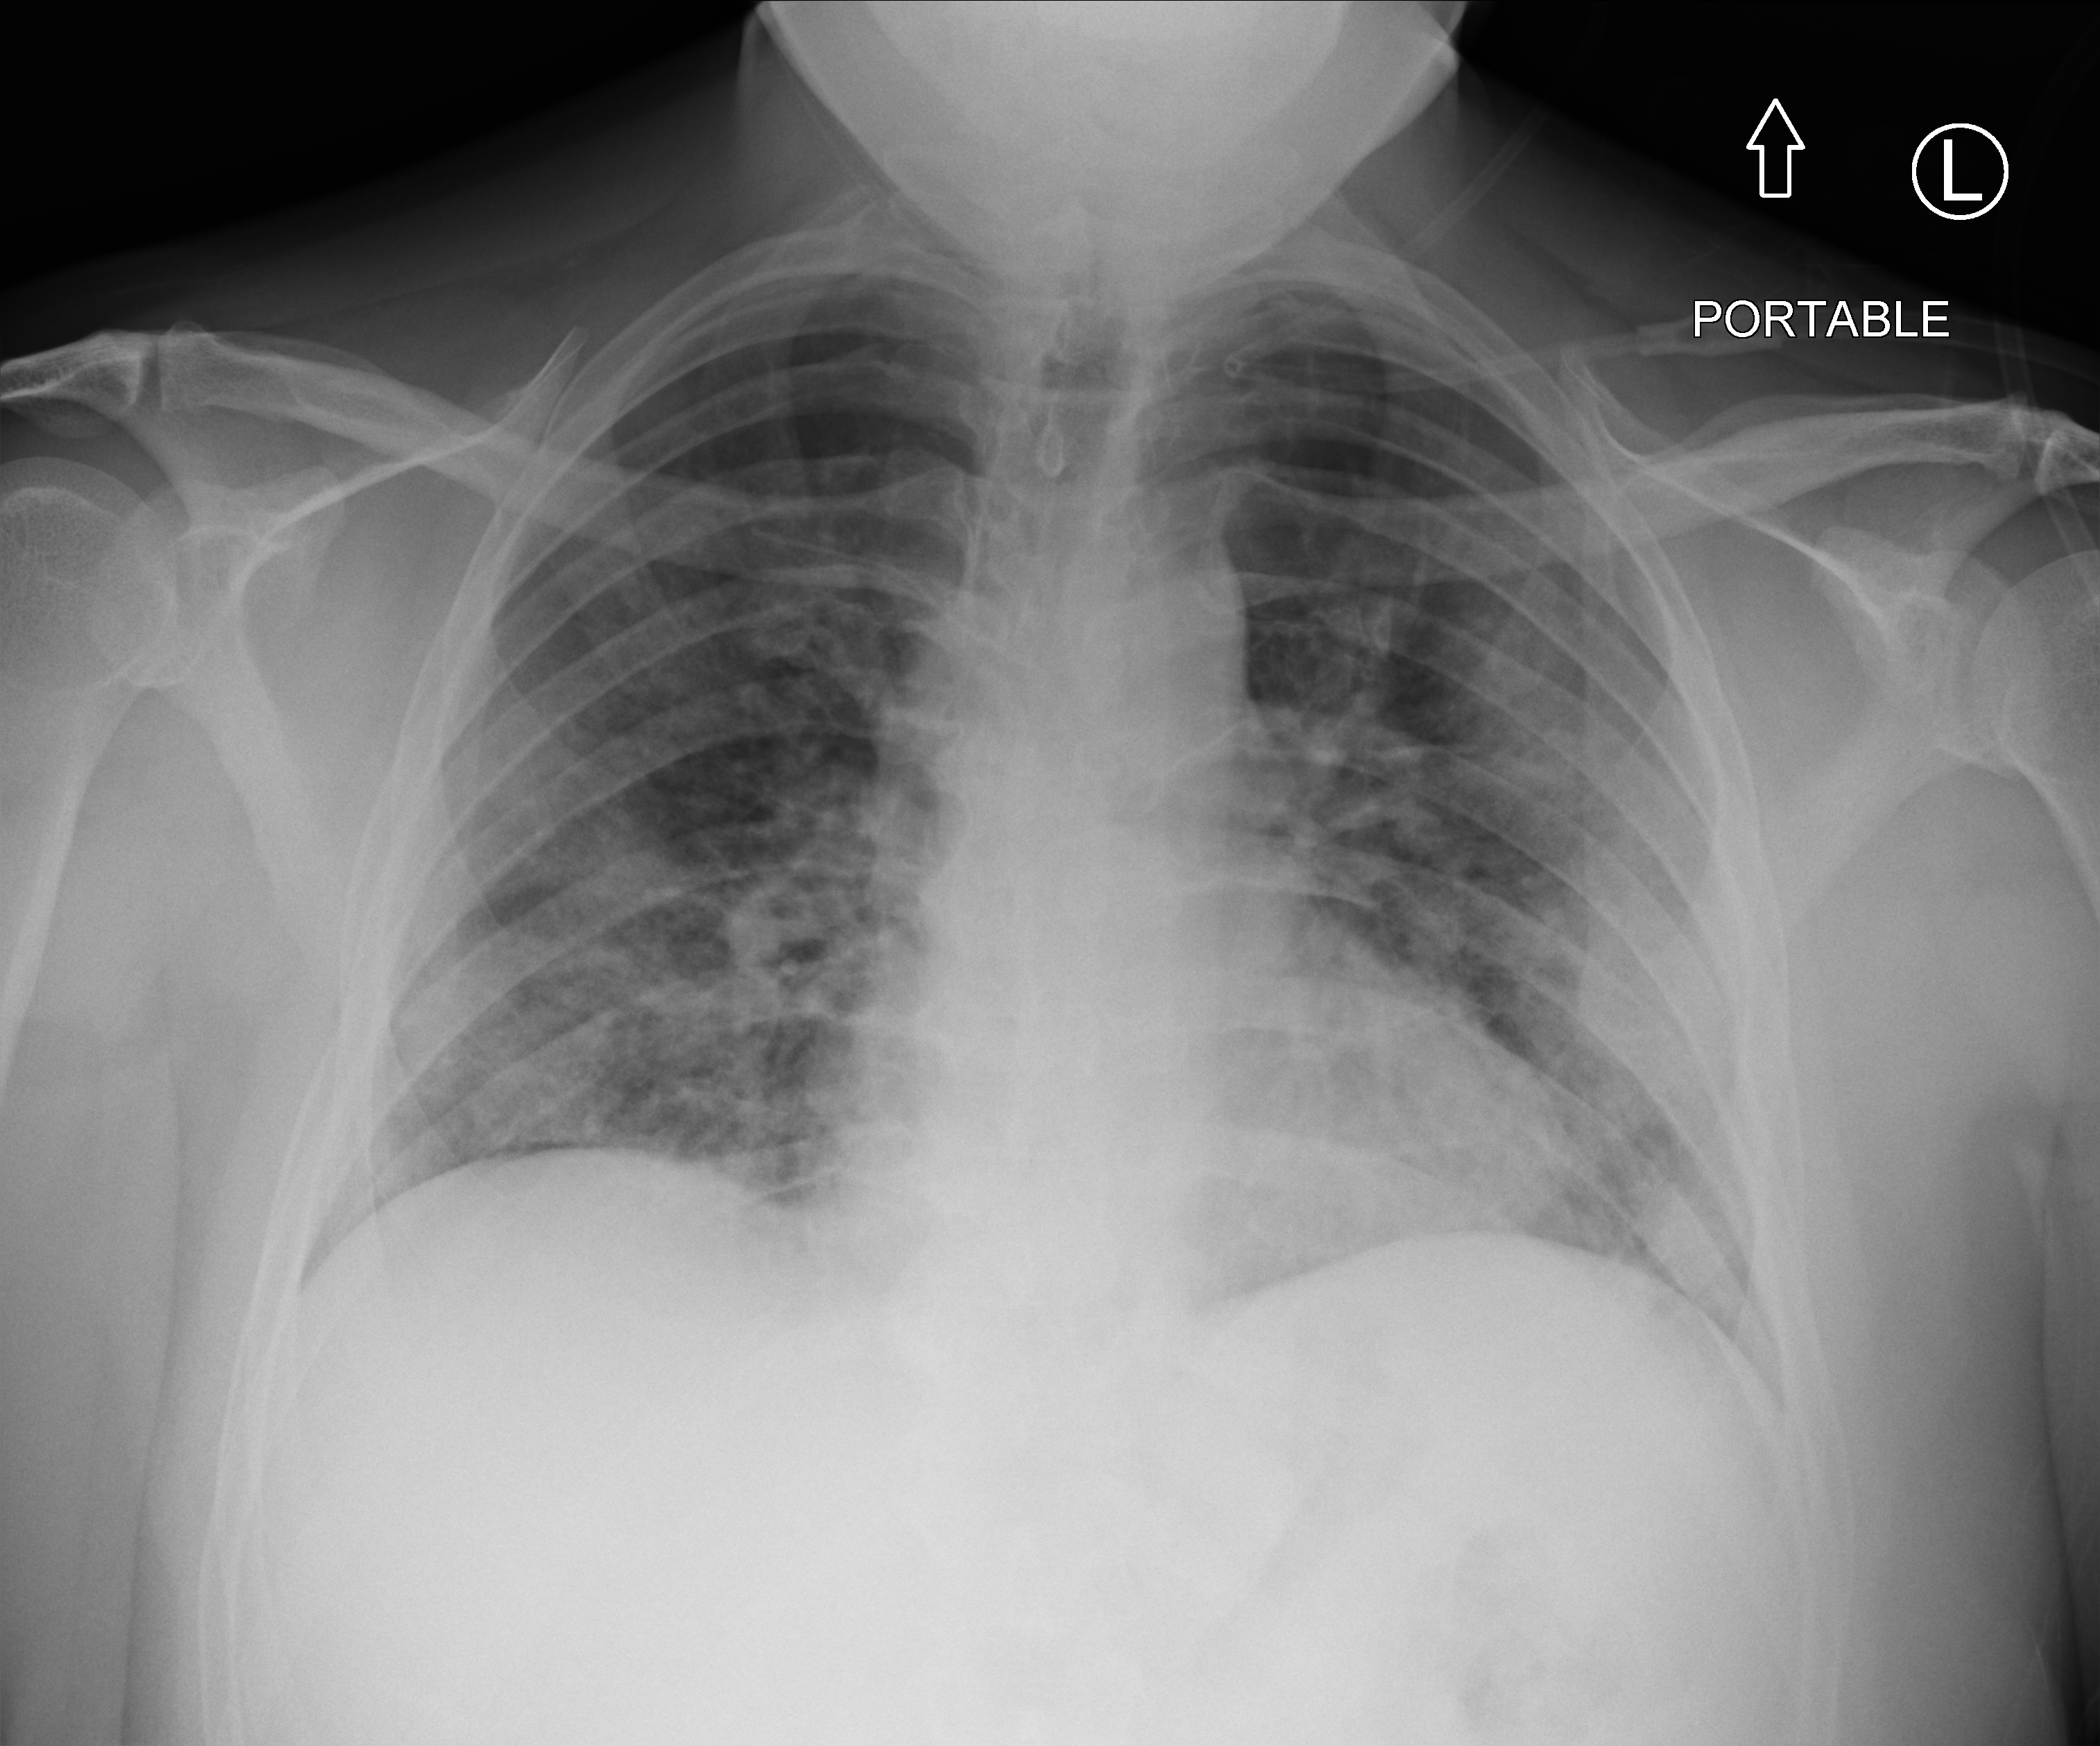
Portable chest radiograph. Male patient hospitalised with COVID-19, age 18–59 years.
Hospital-stay facts (about this admission, not read from this image; timing relative to this image not recorded):
- admitted to intensive care during this hospital stay: no